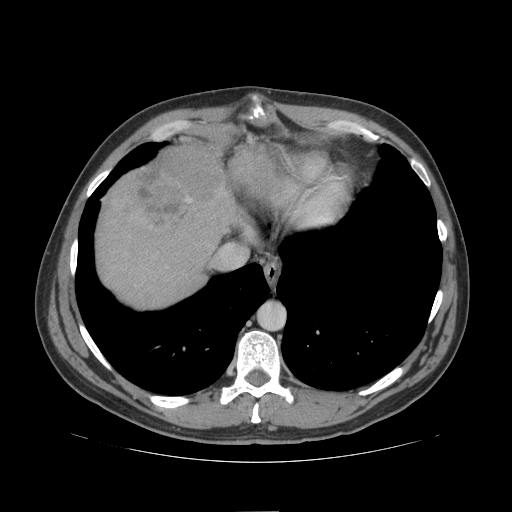
Contrast-enhanced abdominal CT (liver protocol), one axial slice; position 90 of 109 along the scan axis; reconstruction kernel STANDARD; soft-tissue window (W 400 / L 40 HU); 2.5 mm slice thickness; 512 × 512 image matrix, field of view 420 × 420 mm. Case-level facts recorded for this patient, not image findings: diagnosis: hepatocellular carcinoma (patient treated with transarterial chemoembolisation; whether this scan precedes or follows treatment is not stated here); TNM stage (as recorded): Stage-IIIB; Child-Pugh class: A; tumour differentiation: poorly differentiated; tumour nodularity: multinodular.
Annotated regions visible in this slice (semi-automatic segmentation, software-assisted and operator-edited):
- liver parenchyma outside the tumour (the mass and vessels are separate outlines, so this box may not span the whole liver): bounding box (x1, y1, x2, y2) in pixels: (96, 148, 284, 306)
- mass: (105, 138, 226, 234)